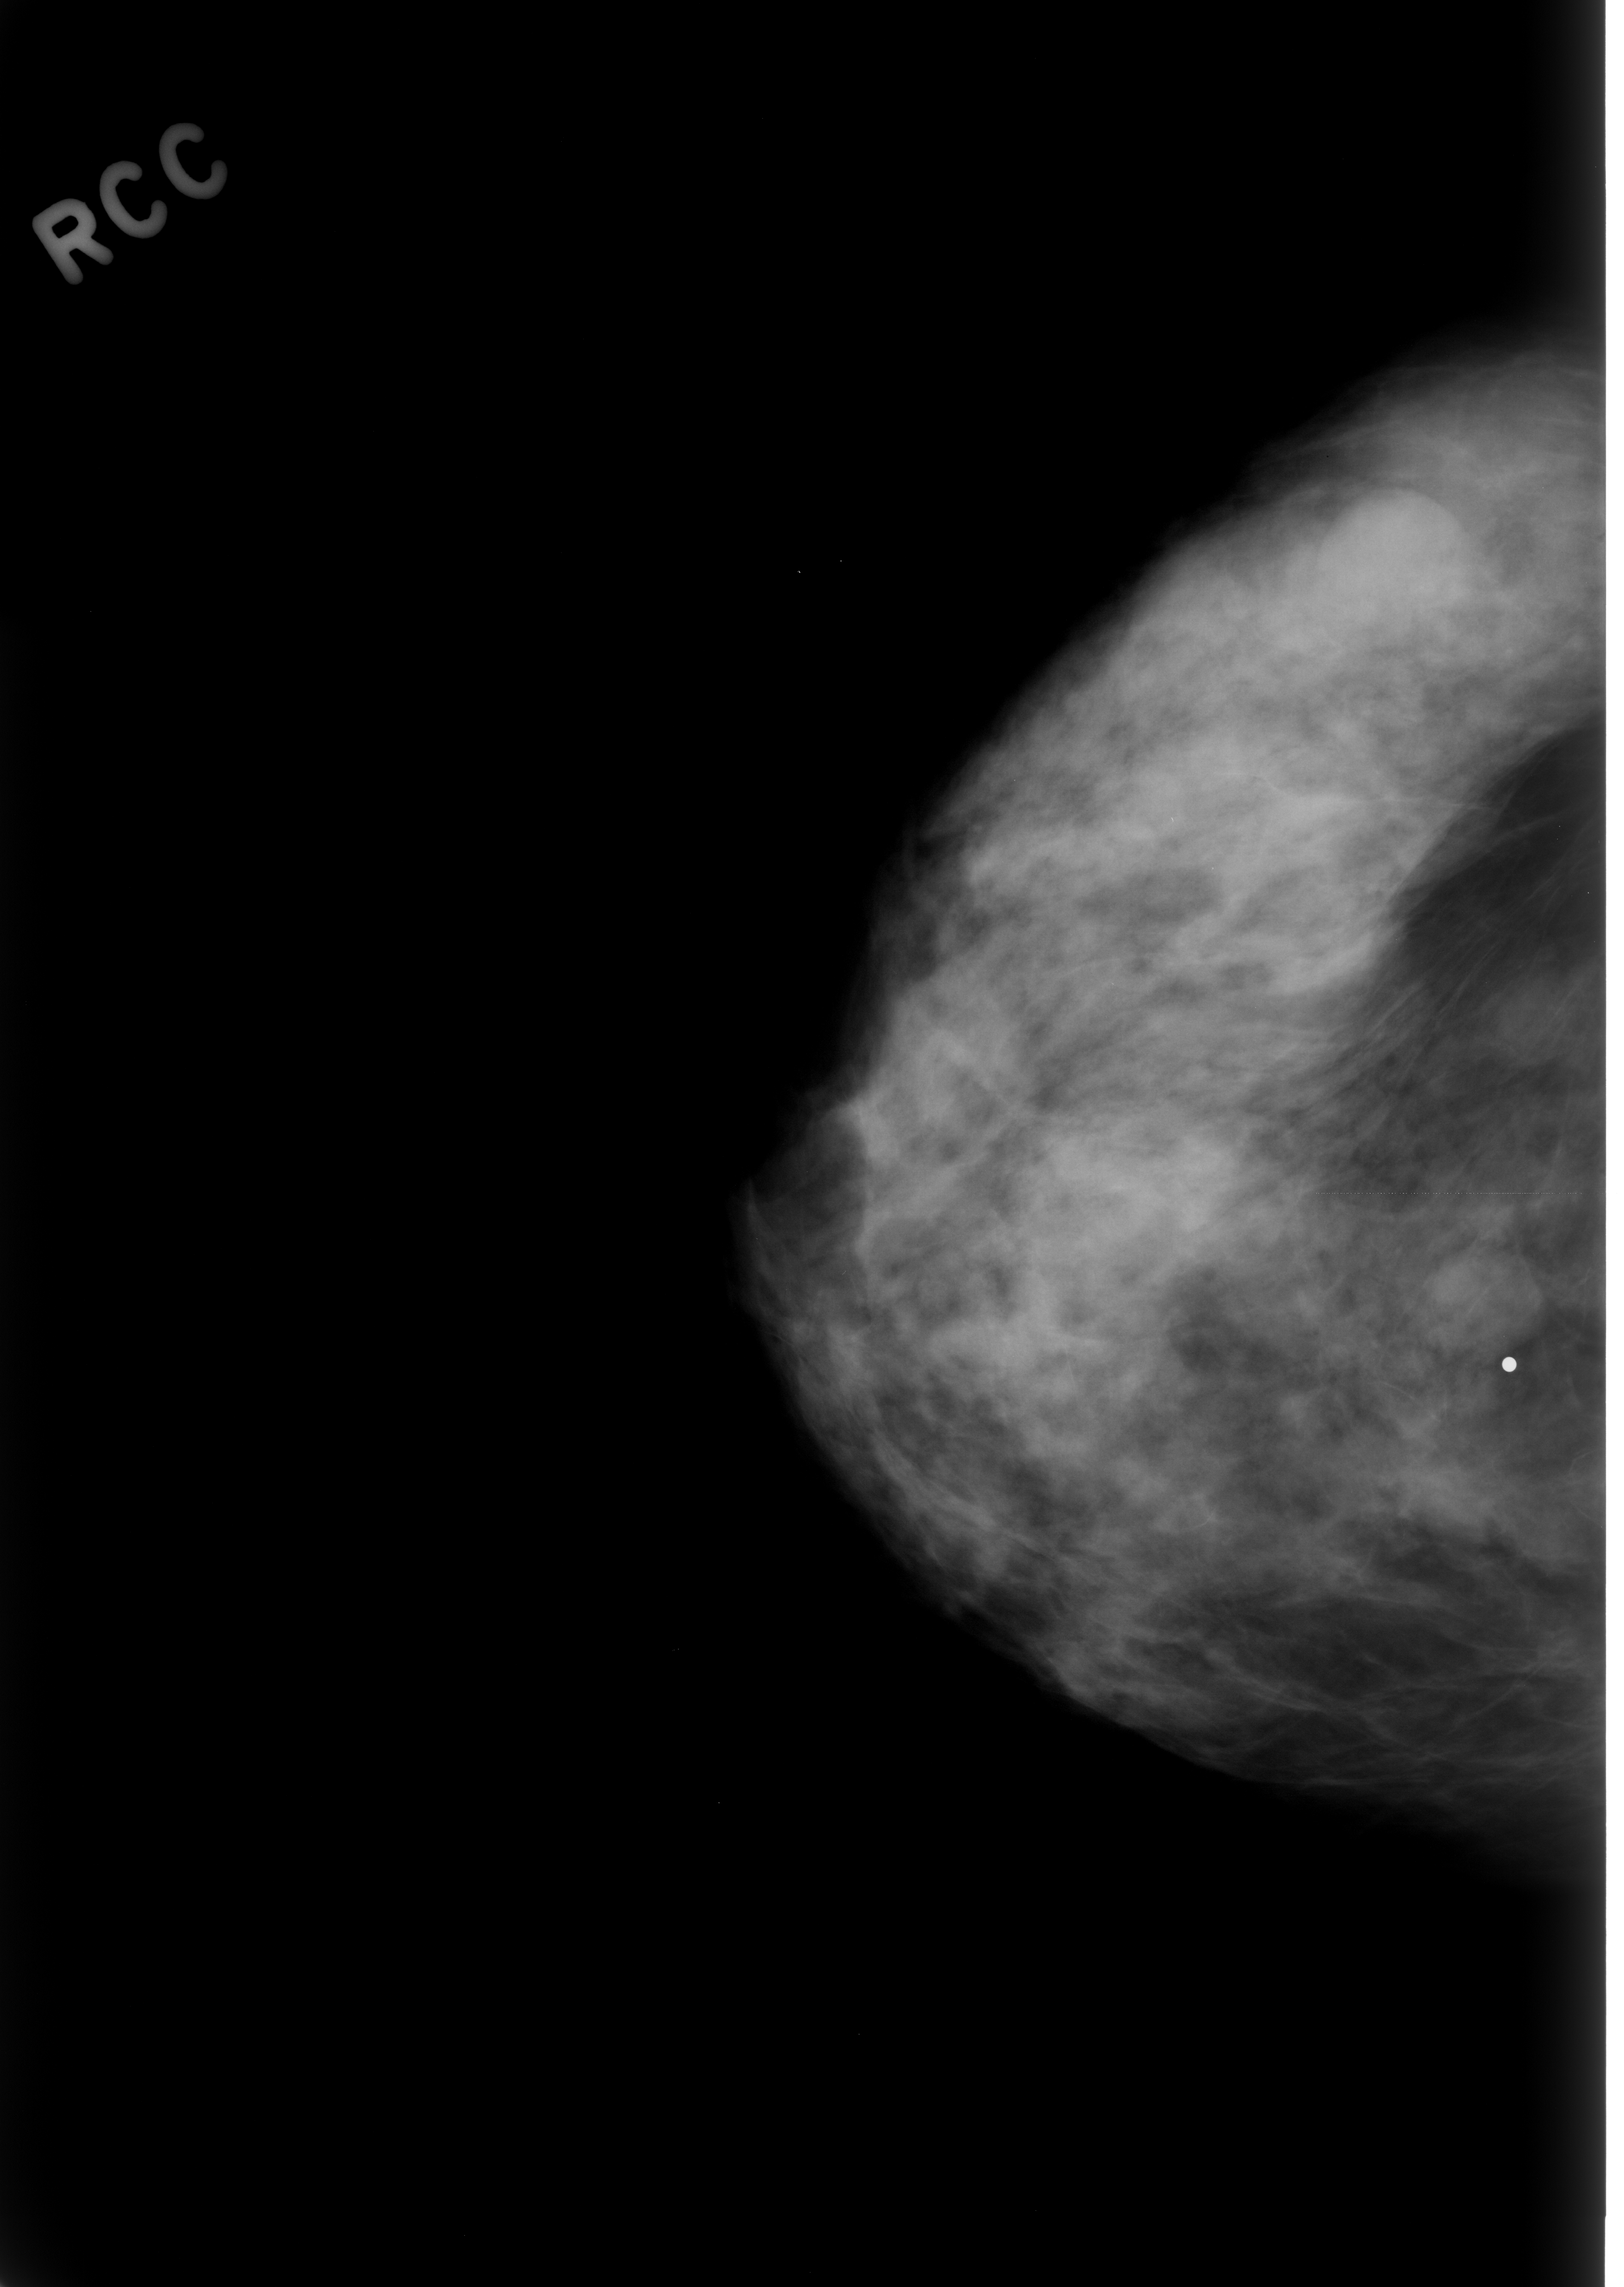
Digitized screen-film mammogram, right breast, CC view, breast composition: heterogeneously dense (BI-RADS density category 3 of 4).
Marked abnormality: mass, shape oval, margins obscured; BI-RADS assessment category 3; pathology result (as recorded, not read from the image): benign.